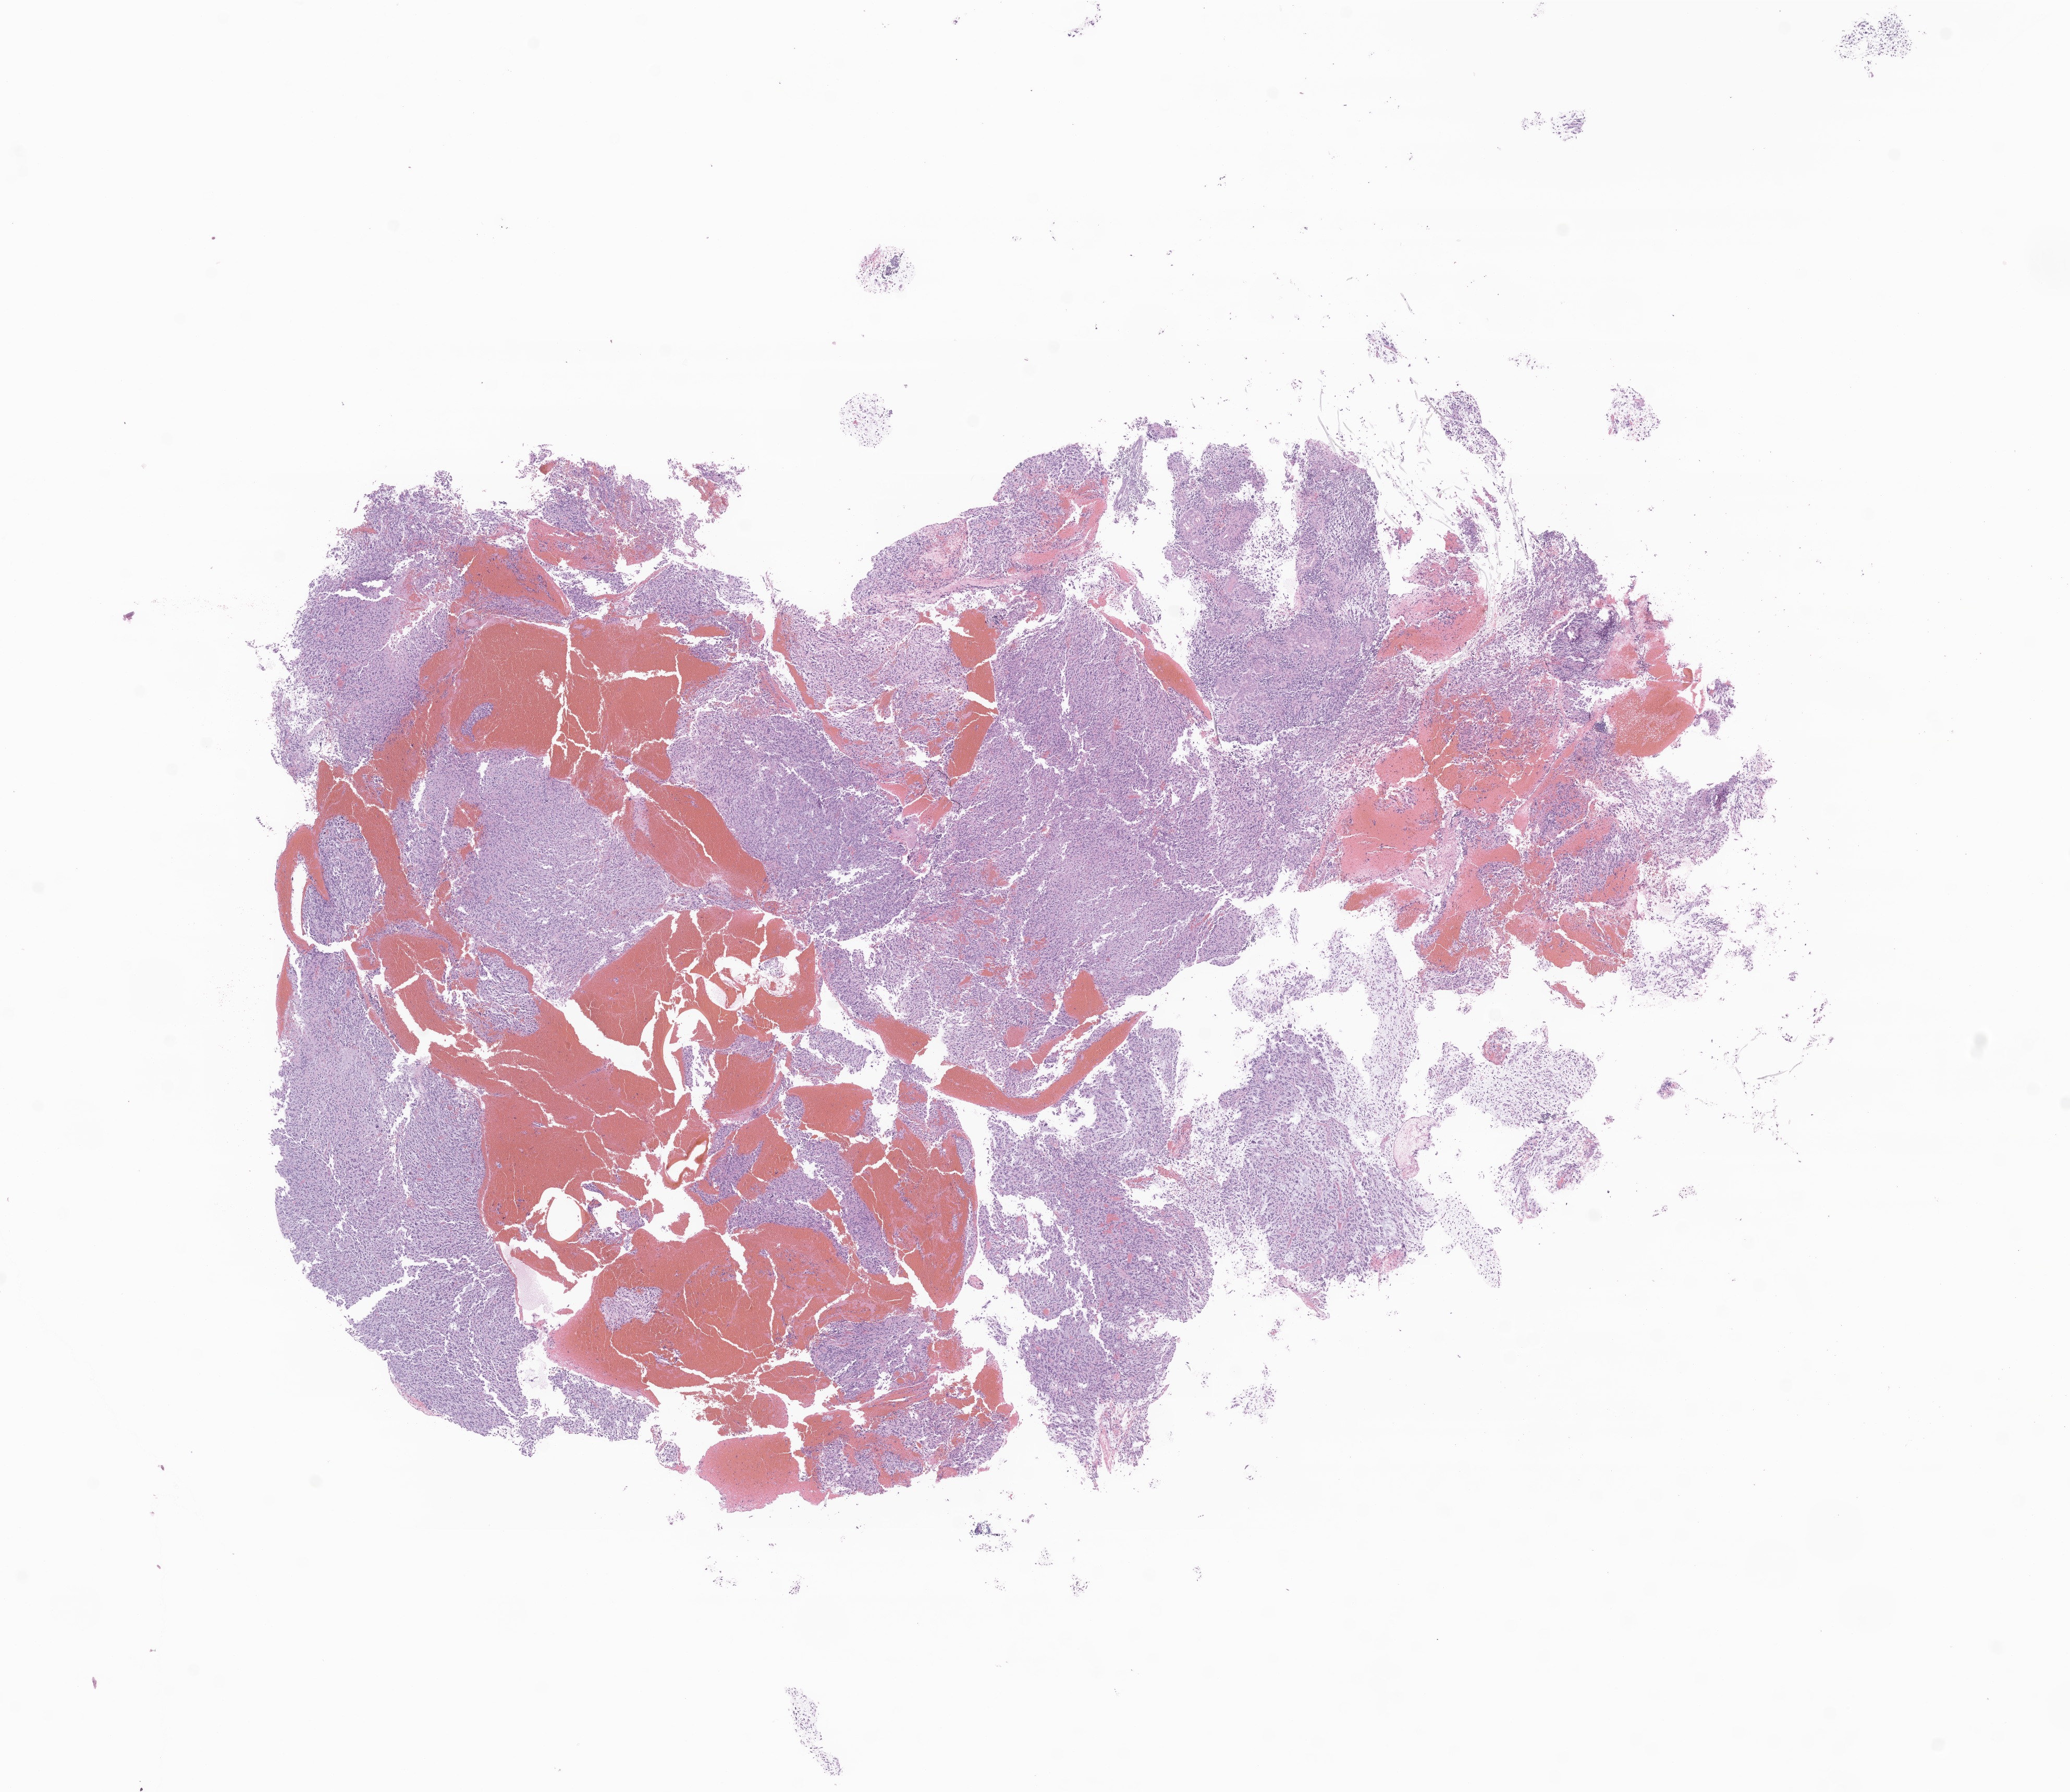
Whole-slide image, hematoxylin and eosin (H&E) stain of tumor tissue from the brain, shown as a low-resolution overview of the whole scanned area (about 16.7 x 14.5 mm), FFPE section. Female patient, age 121 months (10 years 1 month).
• recorded diagnosis: Glioma, malignant